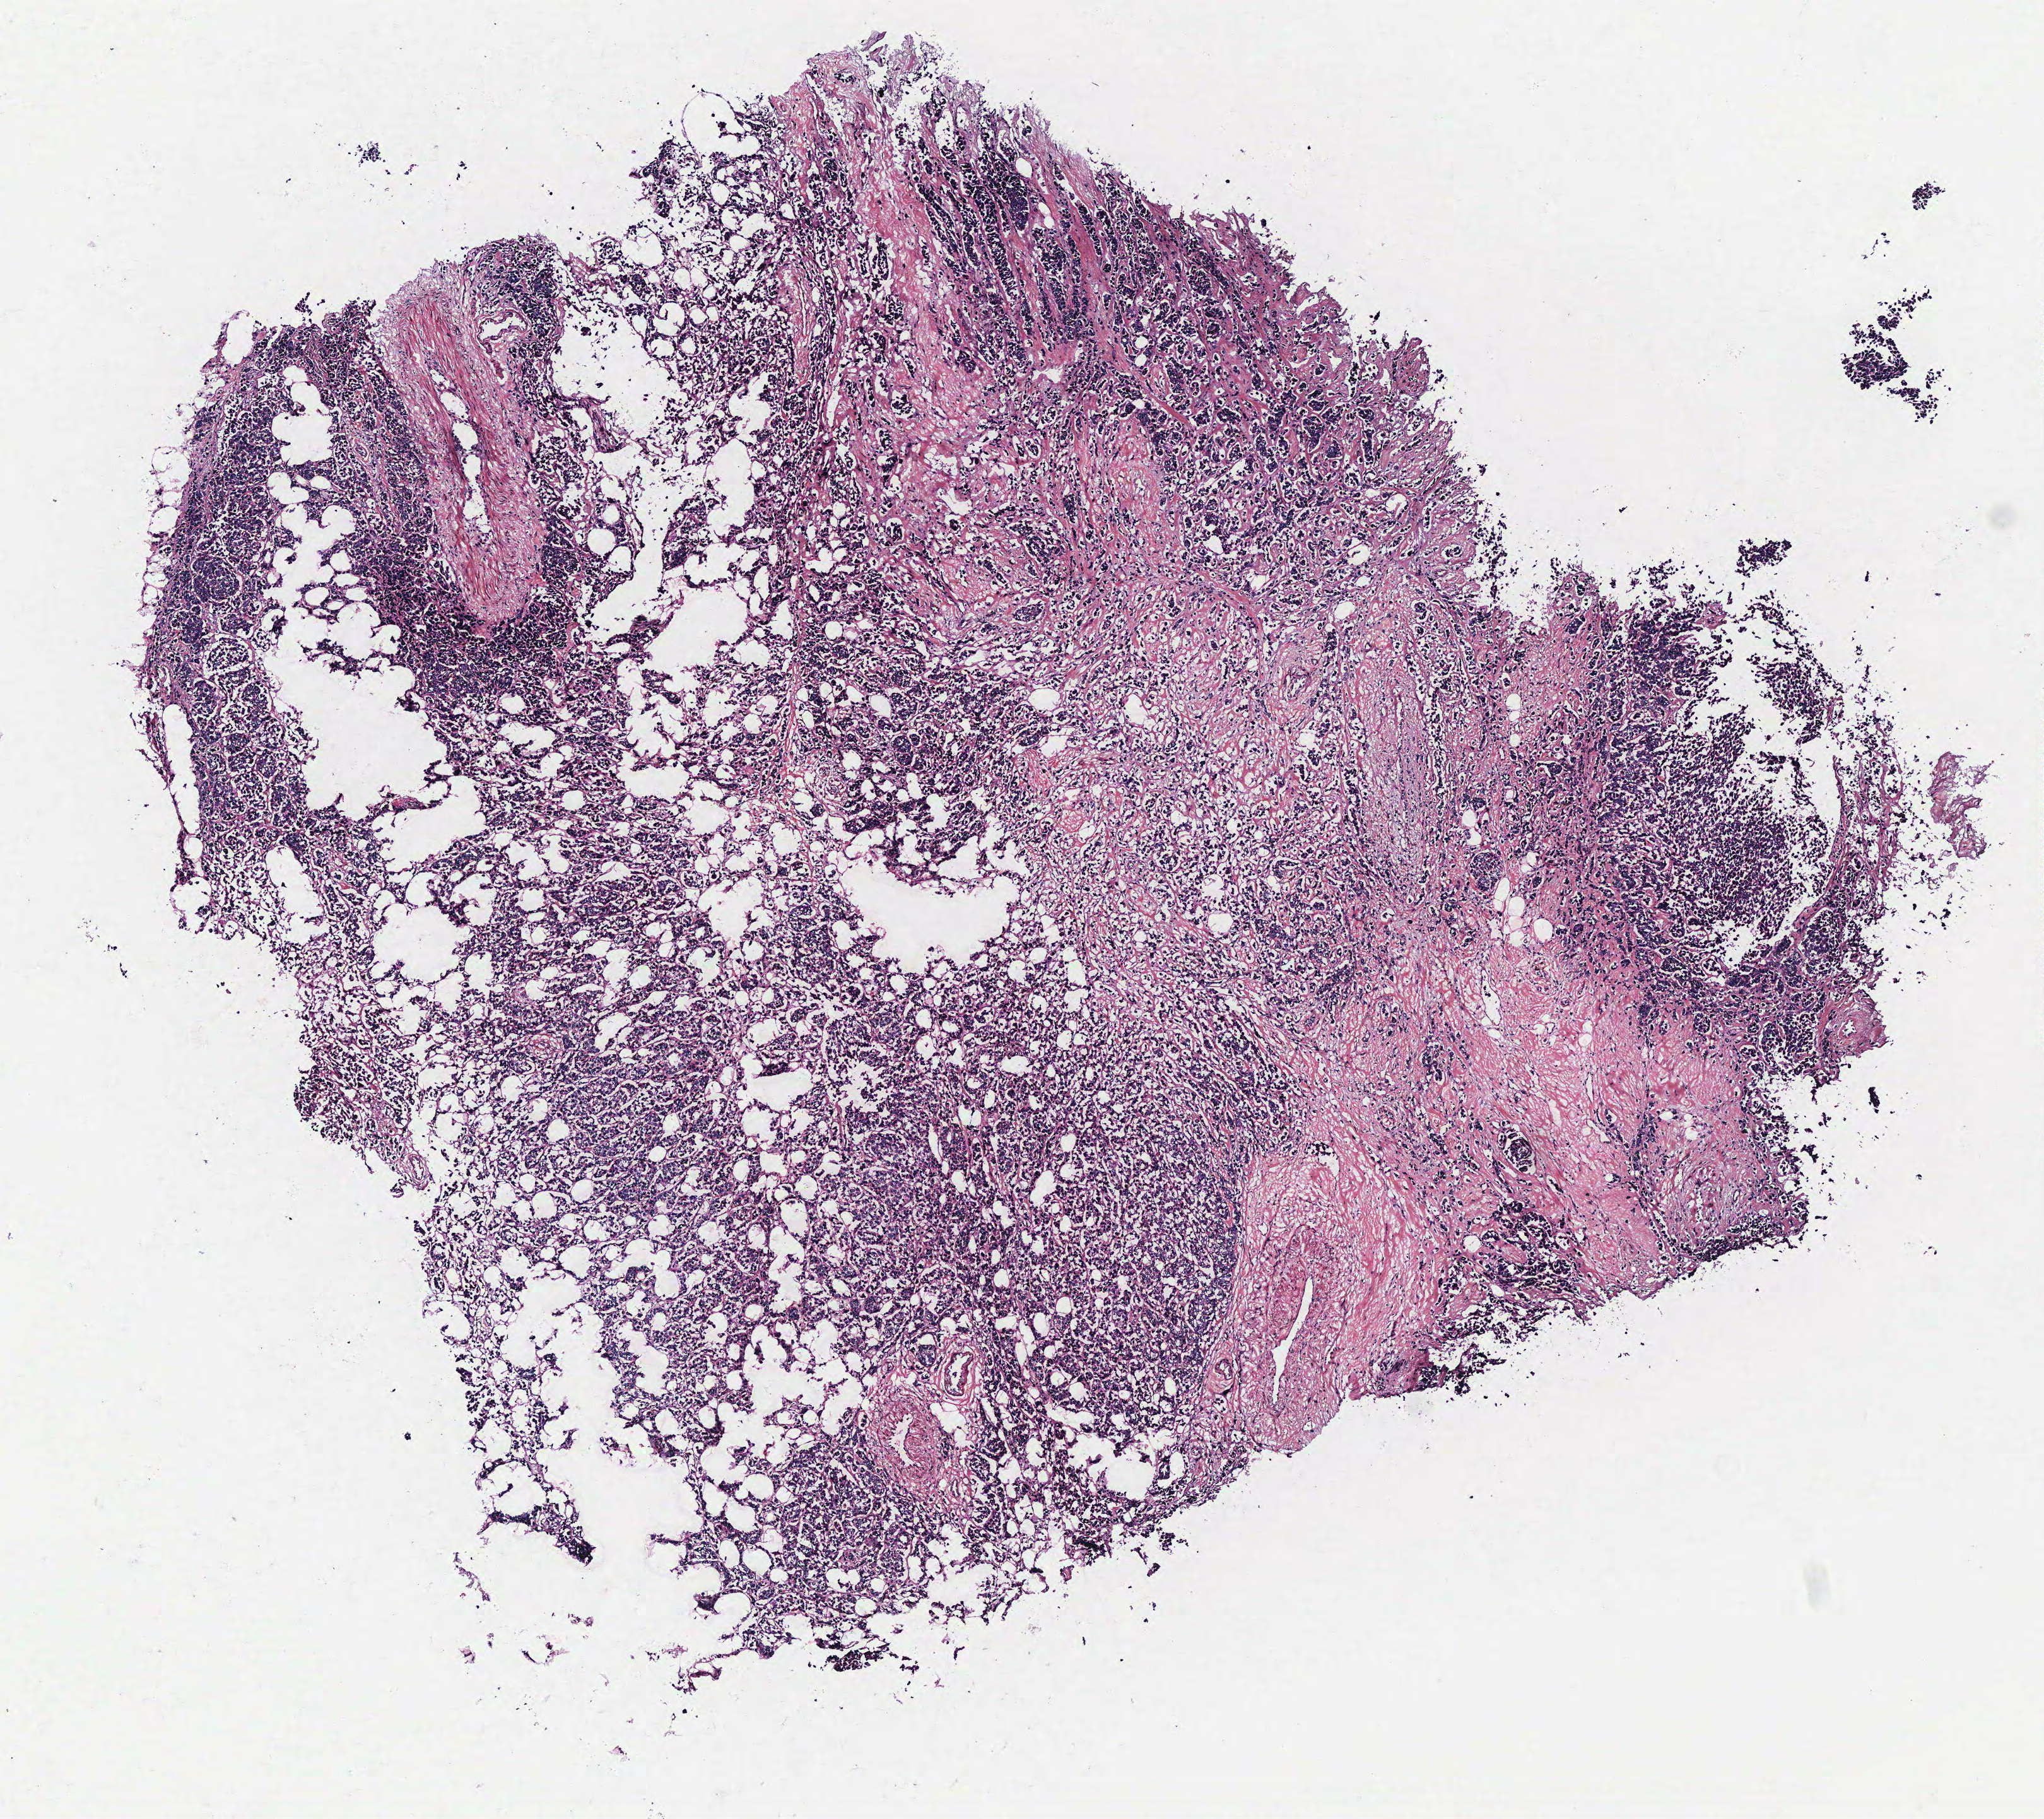
Whole-slide histology image, H&E-stained, low-resolution overview of the scanned area, about 6.5 x 5.8 mm. Patient: female, age 61 years.
Specimen: tumour tissue sample, breast.